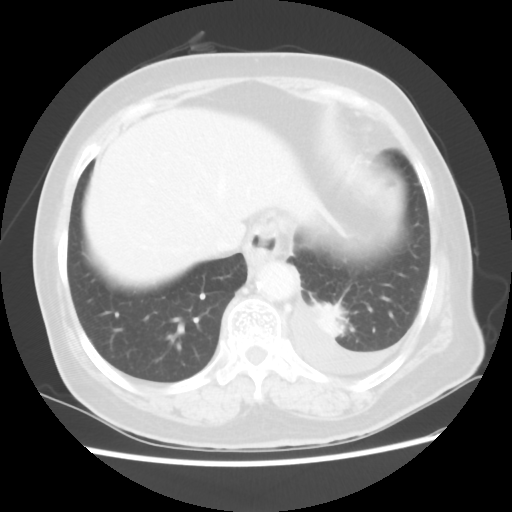
Chest CT, one axial slice; slice 8 of 80 in the series (ordered by position); lung window (W 1500 / L -600 HU); 5 mm slice thickness; 512 × 512 image matrix. Patient: female, 68 years. From the clinical record (not read from this slice): clinical TNM (as recorded): T1c N0 M1.
Annotated regions visible in this slice (bounding box drawn by a radiologist):
- lung tumour (recorded histology: adenocarcinoma): box from (x=311, y=298) to (x=352, y=341) px